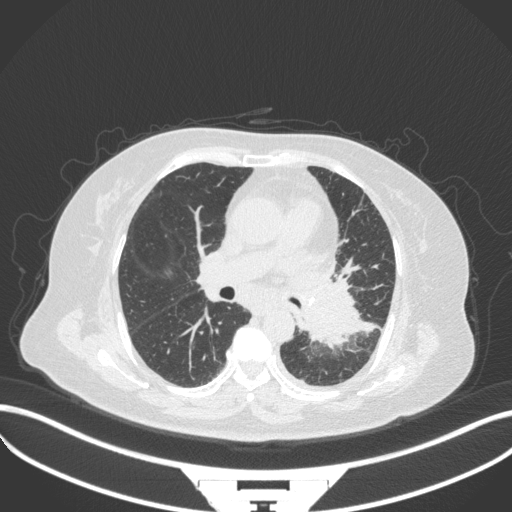
Chest CT, one axial slice. Slice 192 of 328 in the series (ordered by position). Reconstruction kernel B31f. Lung window (W 1500 / L -600 HU). 512 × 512 image matrix, field of view 400 × 400 mm. Patient: female, 69 years. From the clinical record (not read from this slice): clinical TNM (as recorded): T2b N3 M1.
Outlined on this slice (bounding box drawn by a radiologist):
- lung tumour (recorded histology: adenocarcinoma): bounding box (x1, y1, x2, y2) in pixels: (294, 274, 382, 355)